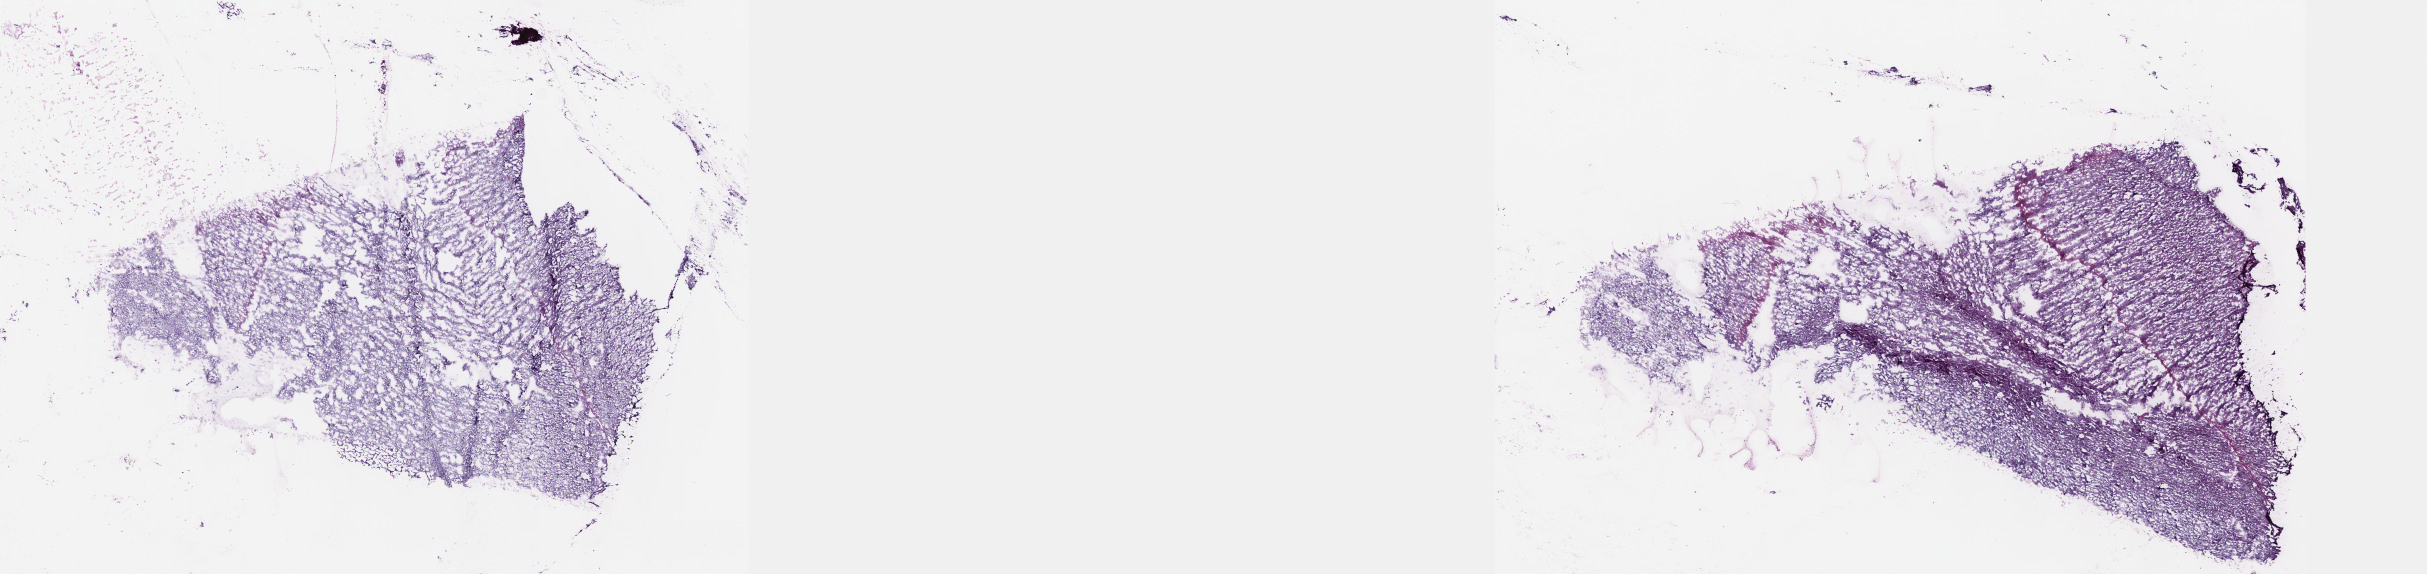
H&E whole-slide image, low-resolution overview of the scanned area, about 19.6 x 4.6 mm (from a 40x scan). Frozen section. Sample: primary tumour, brain. Patient: female, age at initial diagnosis 39 years. Histologic grade: G2 (moderately differentiated). Composition of this section per pathologist review: tumour cells 30%, tumour nuclei 70%, normal cells 10%, stromal cells 60%, necrosis 0%. Infiltration values recorded for this section: lymphocyte infiltration 0%, monocyte infiltration 0%, neutrophil infiltration 0%.
- histologic diagnosis: Astrocytoma, NOS (cerebrum)